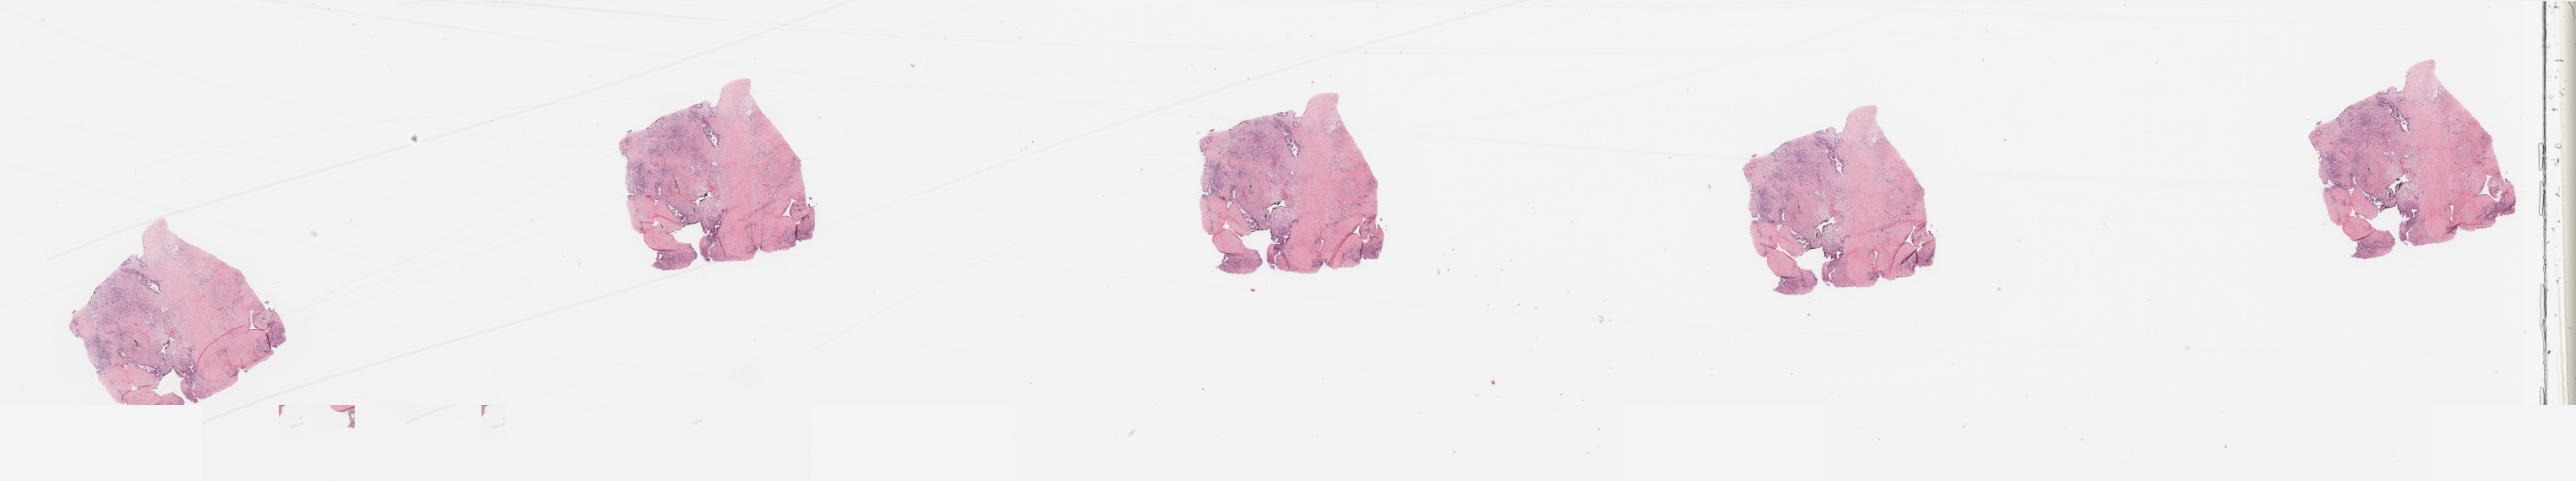
Hematoxylin and eosin (H&E) stained whole-slide image, whole scanned area (about 48.2 x 9.0 mm) shown as a low-resolution overview. Pancreas, tumour tissue. Patient: male, age 77 years. Histologic grade: G2 (moderately differentiated).
Histologic diagnosis: Infiltrating duct carcinoma, NOS. AJCC pathologic stage: III. Primary tumour site (as recorded): head.